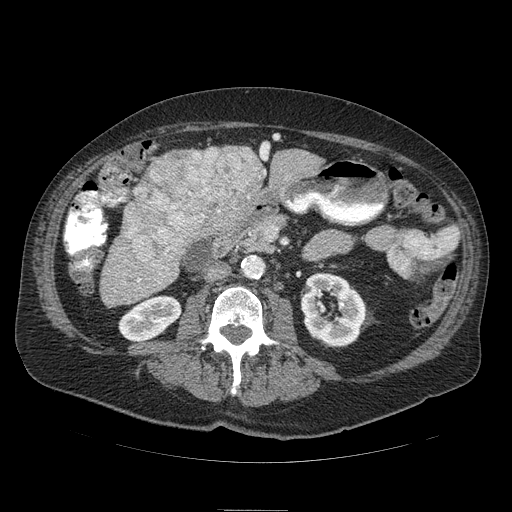
Contrast-enhanced abdominal CT (liver protocol), one axial slice; slice 25 of 103 in the series (ordered by position); reconstruction kernel STANDARD; 120 kVp; soft-tissue window (W 400 / L 40 HU); 512 × 512 image matrix, field of view 440 × 440 mm. From the clinical record (not read from this slice): diagnosis: hepatocellular carcinoma (patient treated with transarterial chemoembolisation; whether this scan precedes or follows treatment is not stated here); TNM stage (as recorded): Stage-IIIA; Child-Pugh class: B; tumour differentiation: well differentiated; tumour nodularity: multinodular.
Outlined on this slice (semi-automatic segmentation, software-assisted and operator-edited):
- liver parenchyma outside the tumour (the mass and vessels are separate outlines, so this box may not span the whole liver): bounding box [x1, y1, x2, y2] px = [110, 142, 322, 268]
- mass: [126, 143, 268, 268]
- liver vessels: [260, 143, 269, 160]